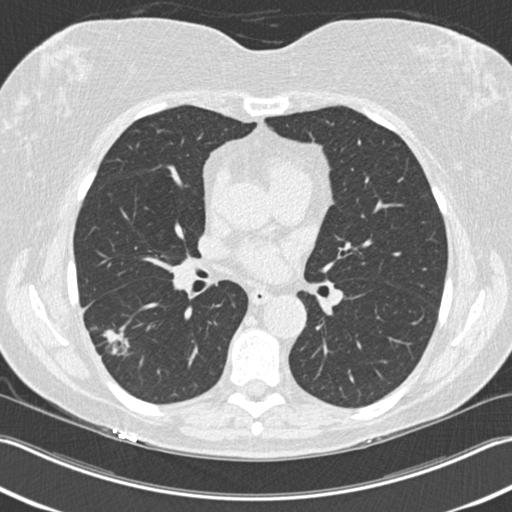
Low-dose screening chest CT, axial slice; baseline annual screen; lung window (W 1500 / L -600 HU); slice 90 of 211 in the series; 512 × 512 image matrix. Female participant, aged 63 years at enrolment. Current smoker at enrolment.
Expert-annotated lung lesion, bounding box [x1, y1, x2, y2] px = [84, 319, 144, 372]. The screening reader recorded 3 non-calcified nodules or masses ≥4 mm on this exam (right upper lobe, right lower lobe, right lower lobe); which of them this box marks is not recorded. Official screen result: positive, change unspecified: nodule(s) >= 4 mm or enlarging nodule(s), mass(es), or other non-specific abnormalities suspicious for lung cancer. Lung cancer was diagnosed 57 days after this screen: bronchiolo-alveolar adenocarcinoma, NOS, right lower lobe, well differentiated (G1), stage IA (AJCC 6th edition), 25 mm at pathology.